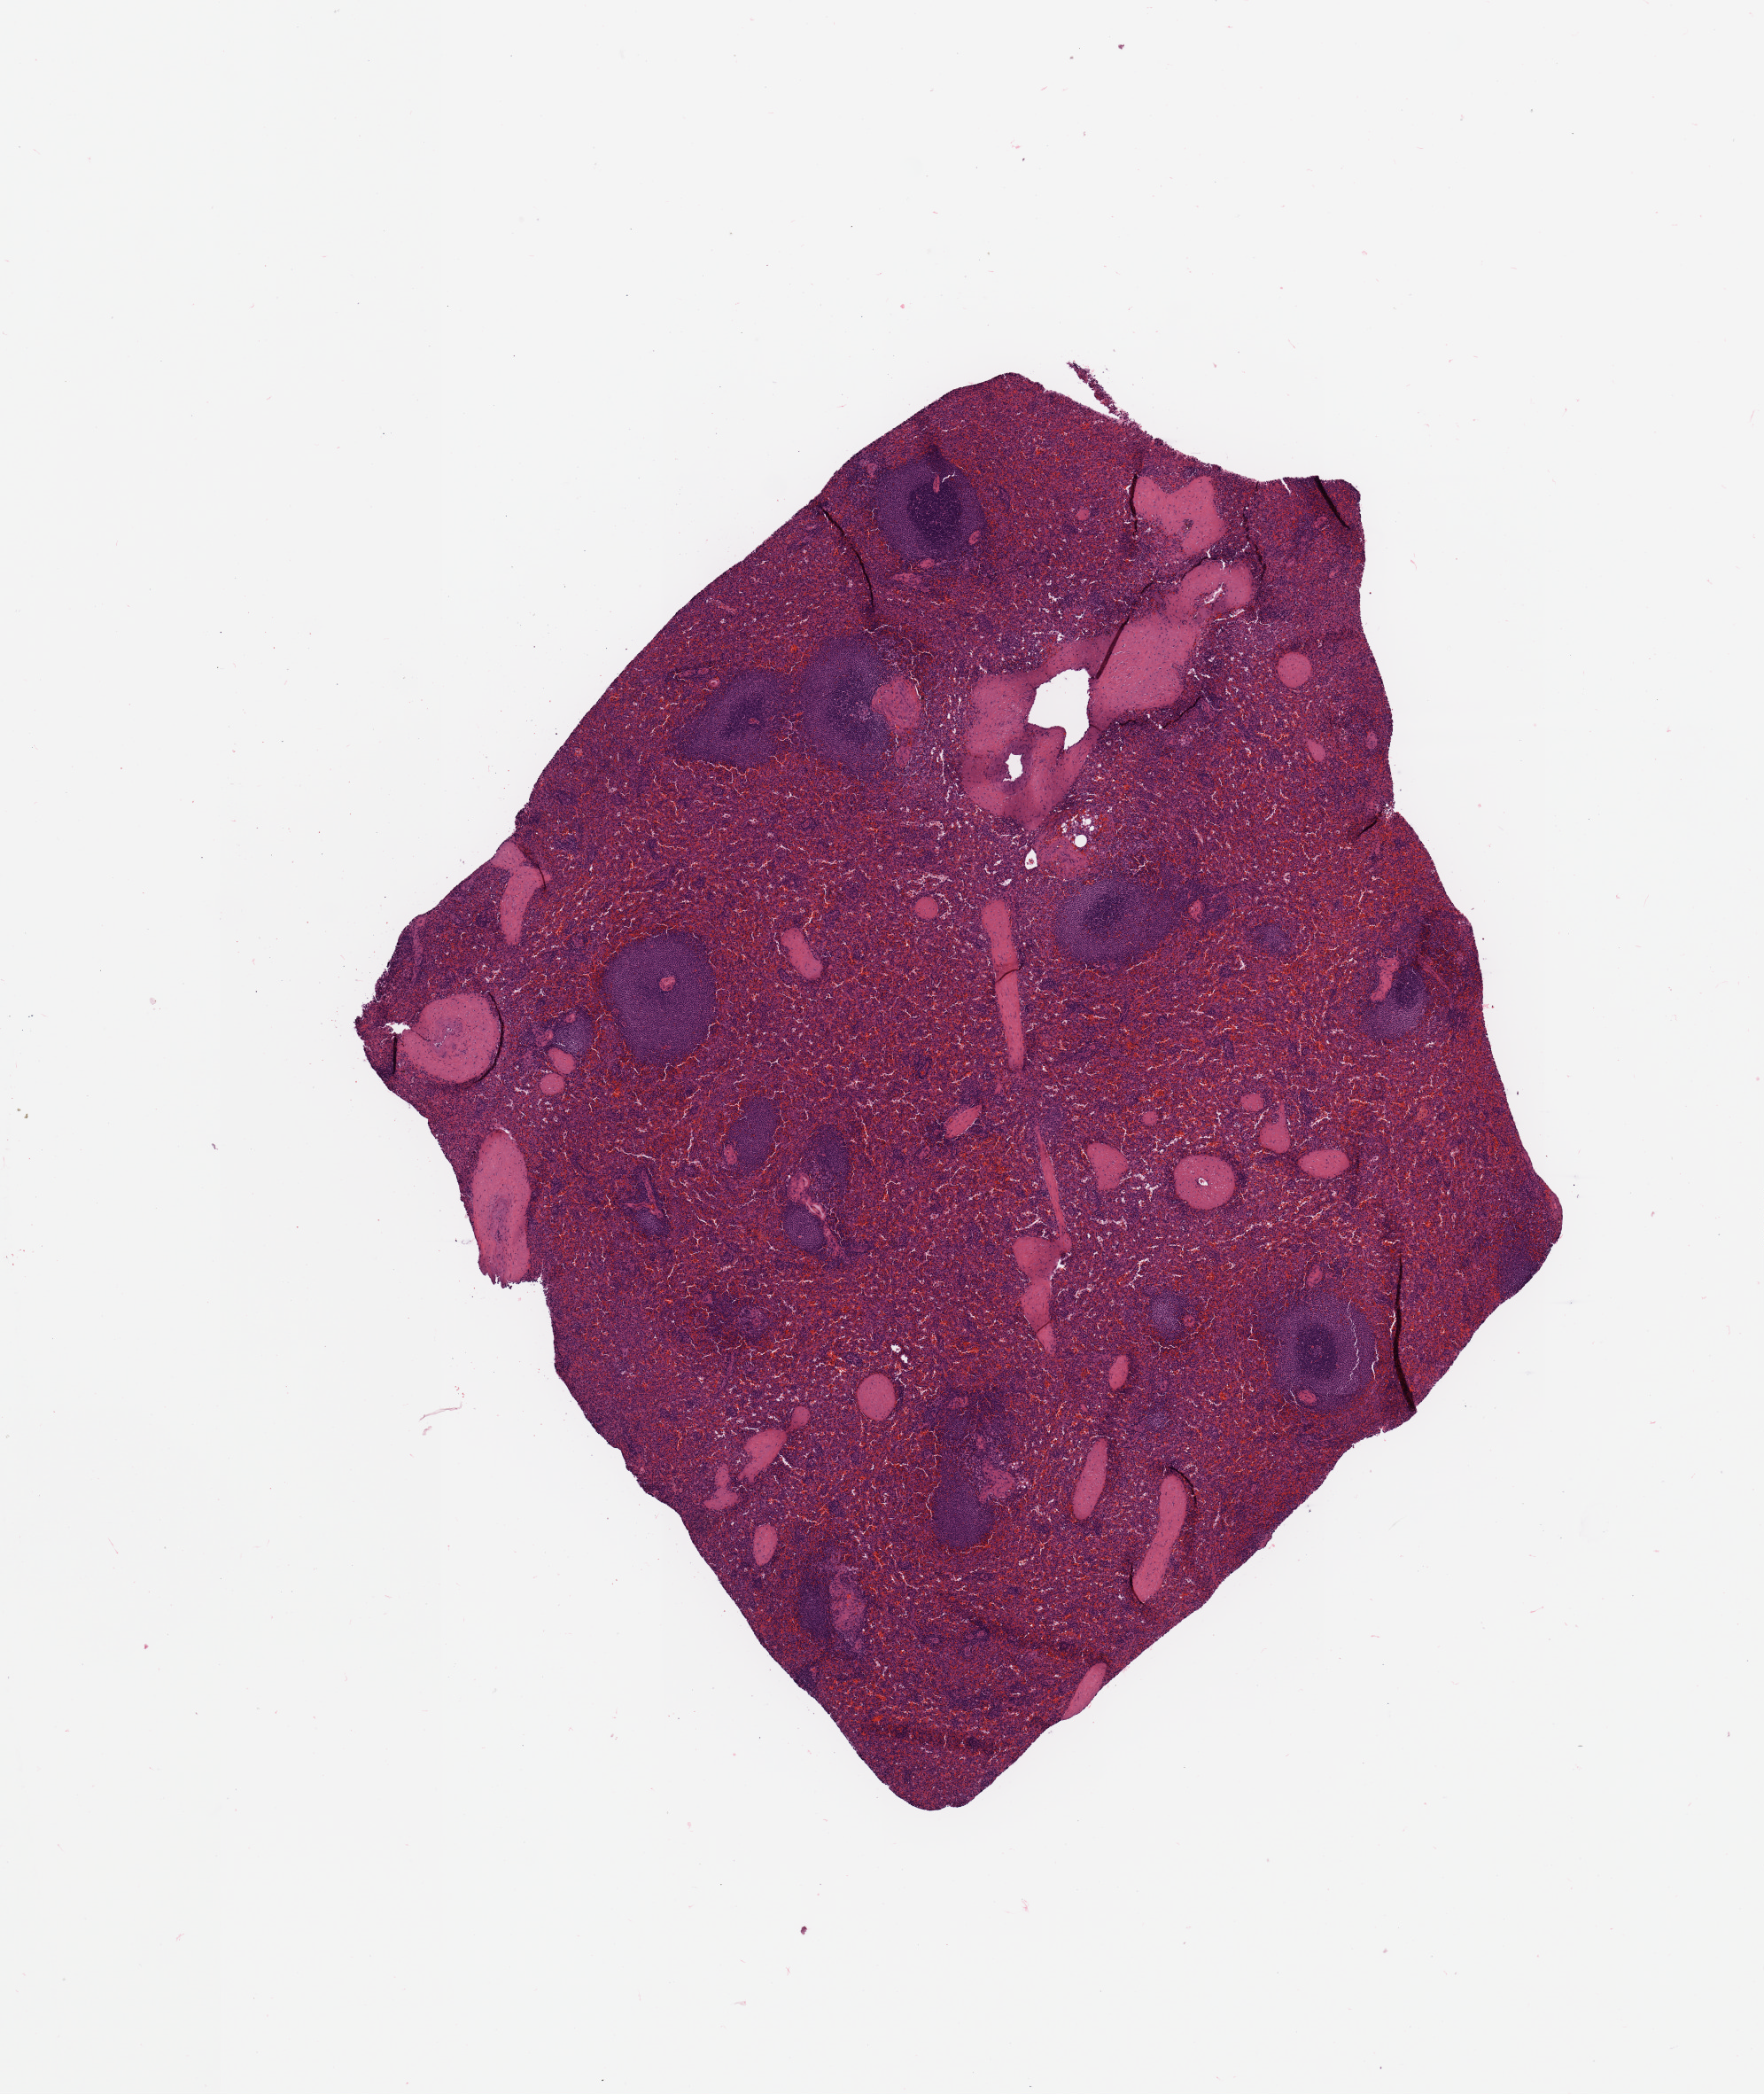
Hematoxylin and eosin (H&E) stained whole-slide image — low-resolution overview of the scanned area, about 7.9 x 9.3 mm (from a 20x scan). Normal (non-tumour) tissue sample, pancreas. 69-year-old male patient.
* this section: normal (non-tumour) tissue from the same patient
* patient diagnosis: Infiltrating duct carcinoma, NOS